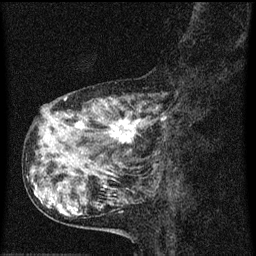
Breast MRI (dynamic contrast-enhanced), one sagittal slice; position 20 of 60 along the scan axis; dynamic contrast-enhanced series, image 2 of 3 at this slice position (ordered by acquisition); 1.5 T; TE 4.2 ms, TR 8 ms; 256 × 256 image matrix, field of view 180 × 180 mm. Female patient, age 55 years.
Structures marked on this image (semi-automatic segmentation, software-assisted and operator-edited):
- analysis volume of interest (the breast-tissue region the enhancement analysis was run in; not a lesion): bounding box <38,92,177,159> (left, top, right, bottom; pixels)
- tumour enhancement mask (voxels above the 70 % enhancement threshold inside the analysis volume of interest): <44,98,159,145>